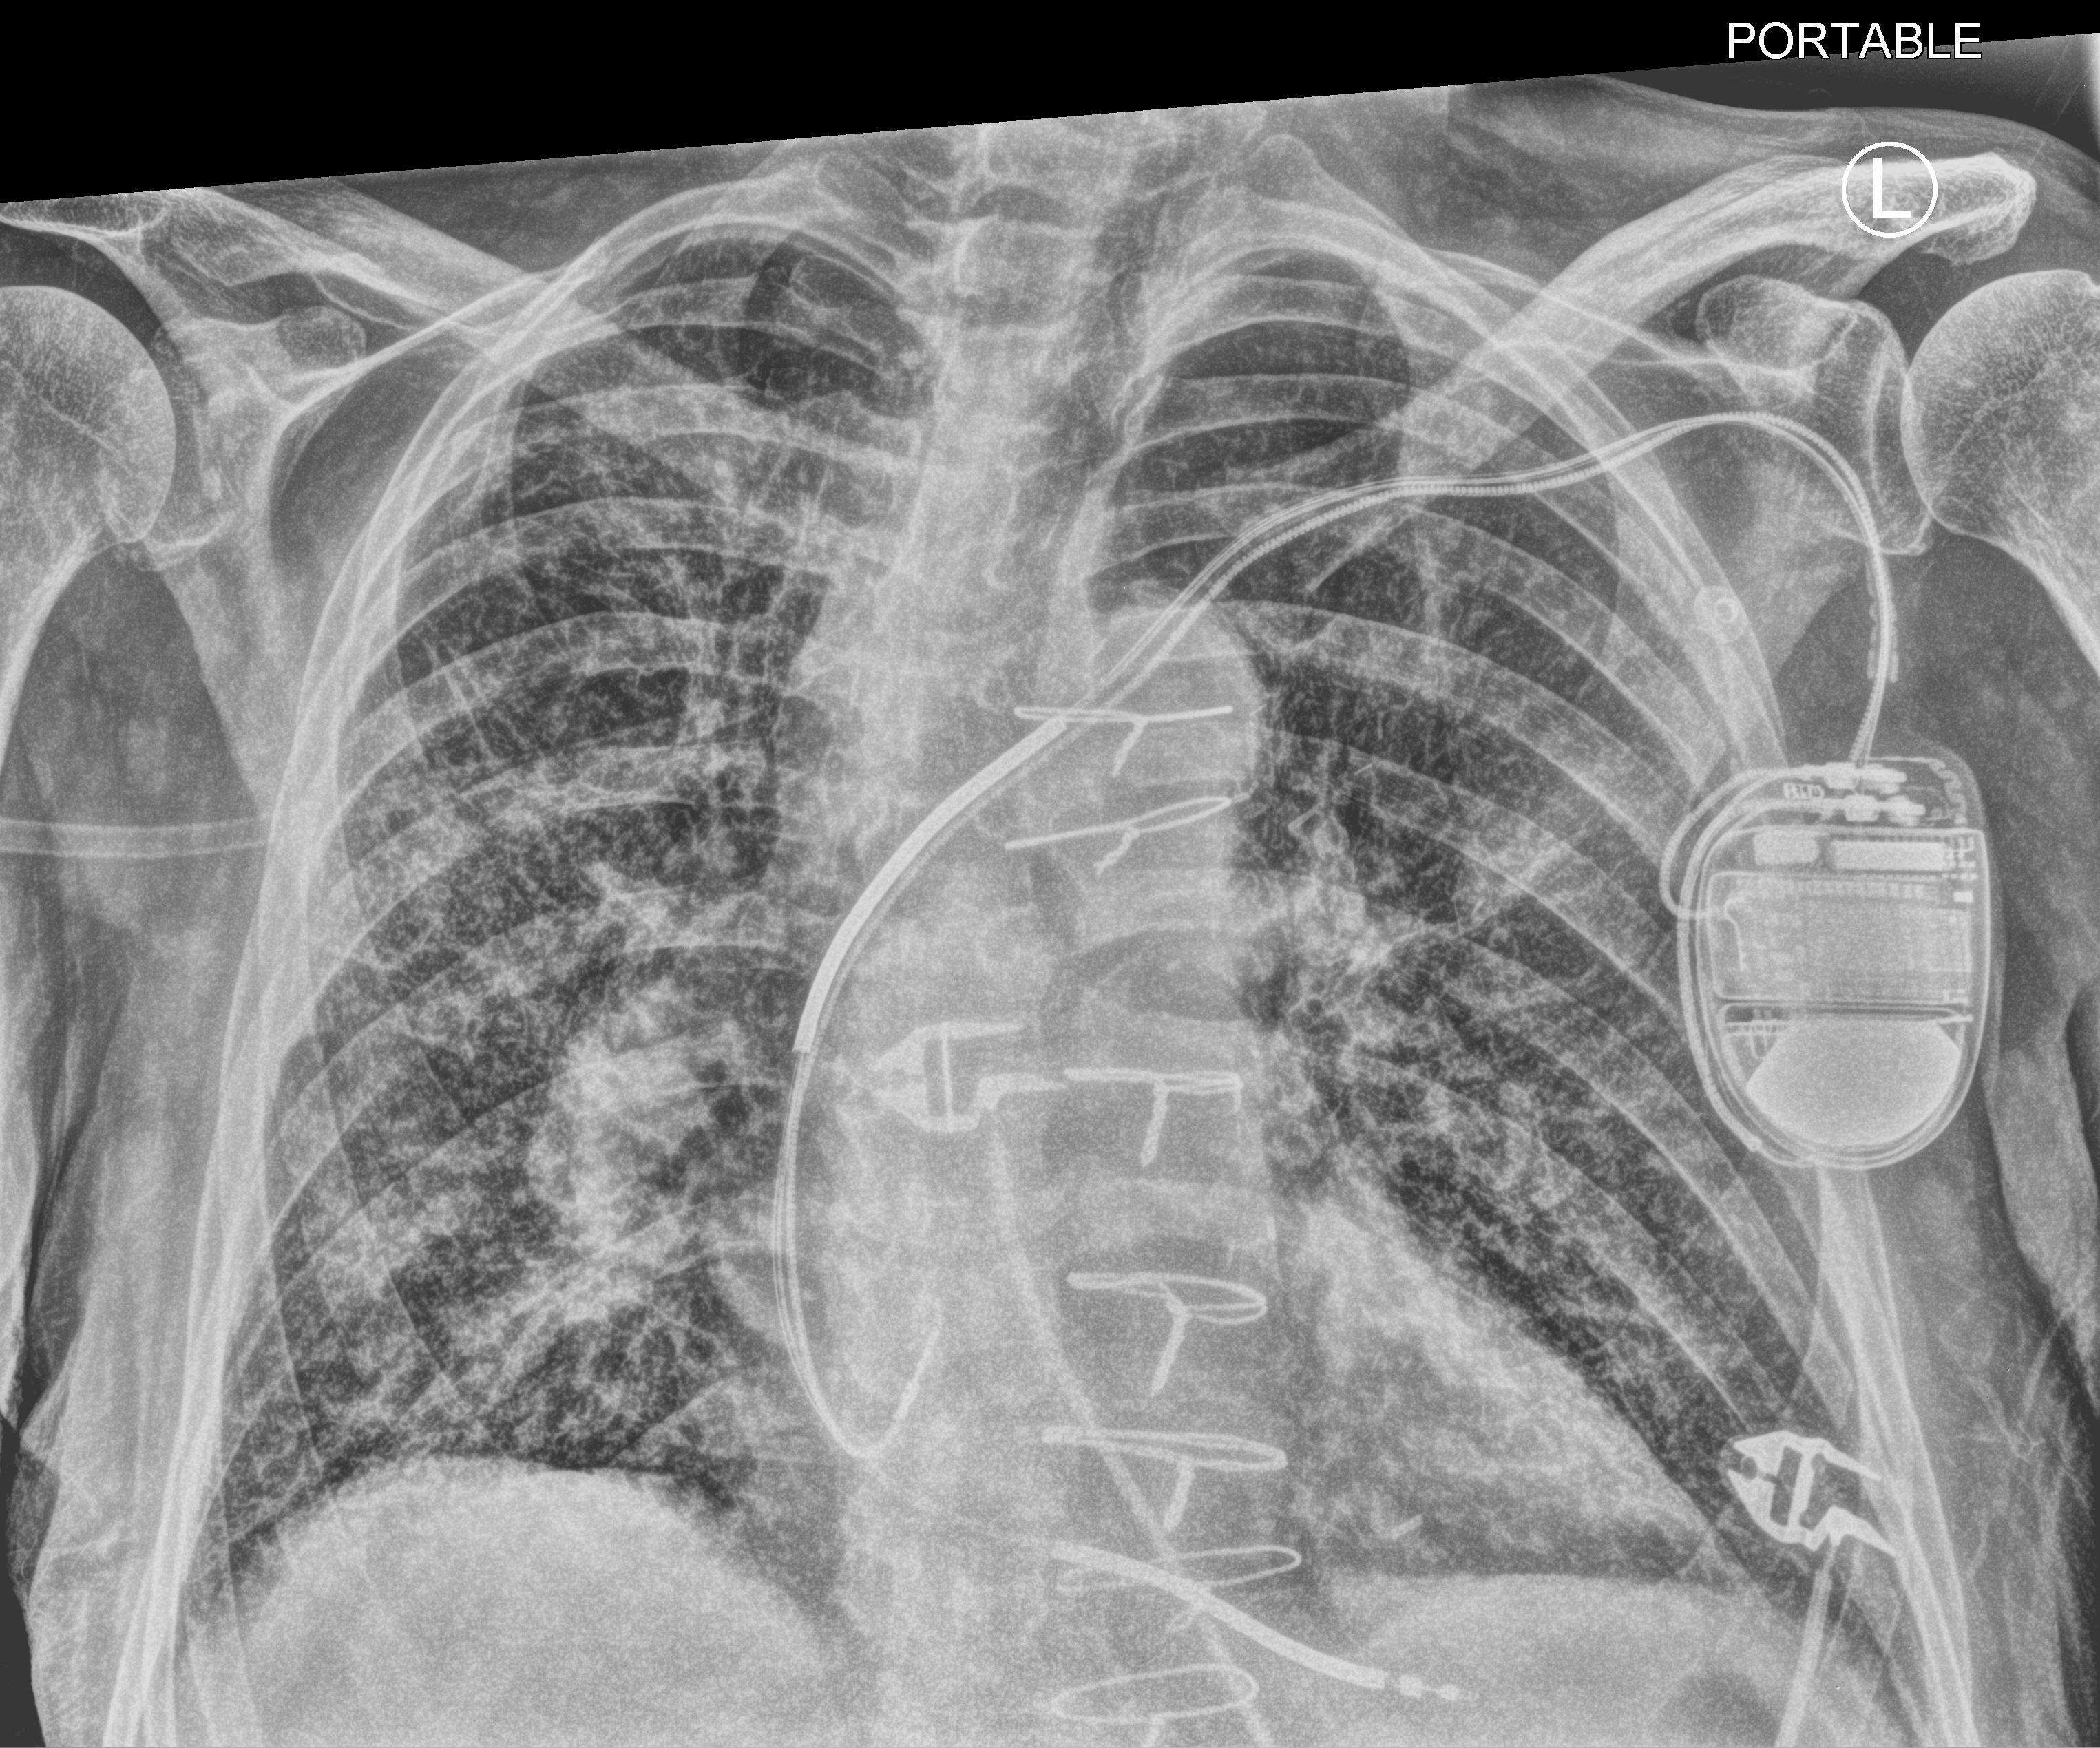
Portable chest radiograph, anteroposterior (AP) projection. Patient hospitalised with COVID-19; male, aged 75–90 years.
From the hospital-stay record, not from the radiograph (when in the stay this image was taken is not recorded):
- length of hospital stay: 10 days
- mechanically ventilated during this hospital stay: no
- diabetes (admission record): no